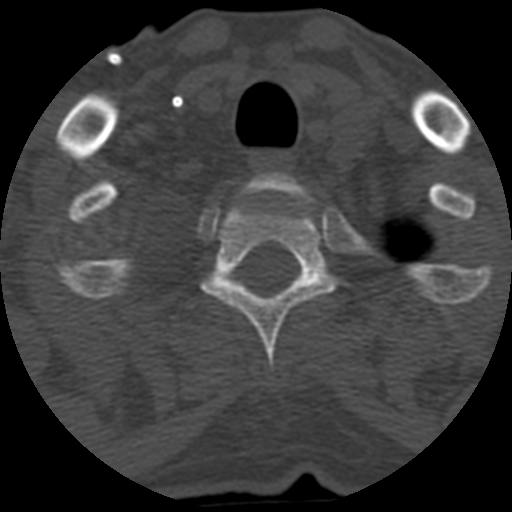
CT including the spine, one axial slice. Slice 505 of 708 in the series (ordered by position). Reconstruction kernel STANDARD. One of 3 acquisitions stored at this slice position. Bone window (W 1800 / L 400 HU). 1.25 mm slice thickness. 512 × 512 image matrix, field of view 160 × 160 mm. Patient age 55 years. From the clinical record (not read from this slice): primary cancer: colon.
Structures marked on this image (semi-automatic segmentation, software-assisted and operator-edited):
- T1 vertebra: bounding box (x1, y1, x2, y2) in pixels: (248, 173, 301, 193)
- T2 vertebra: (201, 201, 337, 371)